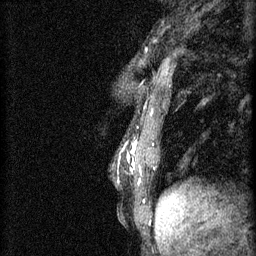
Breast MRI (dynamic contrast-enhanced), one sagittal slice. Position 18 of 60 along the scan axis. 3 images stored at this slice position (order not interpretable as contrast timing). 1.5 T. TE 4.2 ms, TR 11 ms. 2 mm slice thickness. 256 × 256 image matrix, field of view 180 × 180 mm. Female patient, age 37 years.
Outlined on this slice (semi-automatically segmented with operator editing):
- analysis volume of interest (the breast-tissue region the enhancement analysis was run in; not a lesion): bounding box <118,120,157,181> (left, top, right, bottom; pixels)
- tumour enhancement mask (voxels above the 70 % enhancement threshold inside the analysis volume of interest): <128,140,137,171>